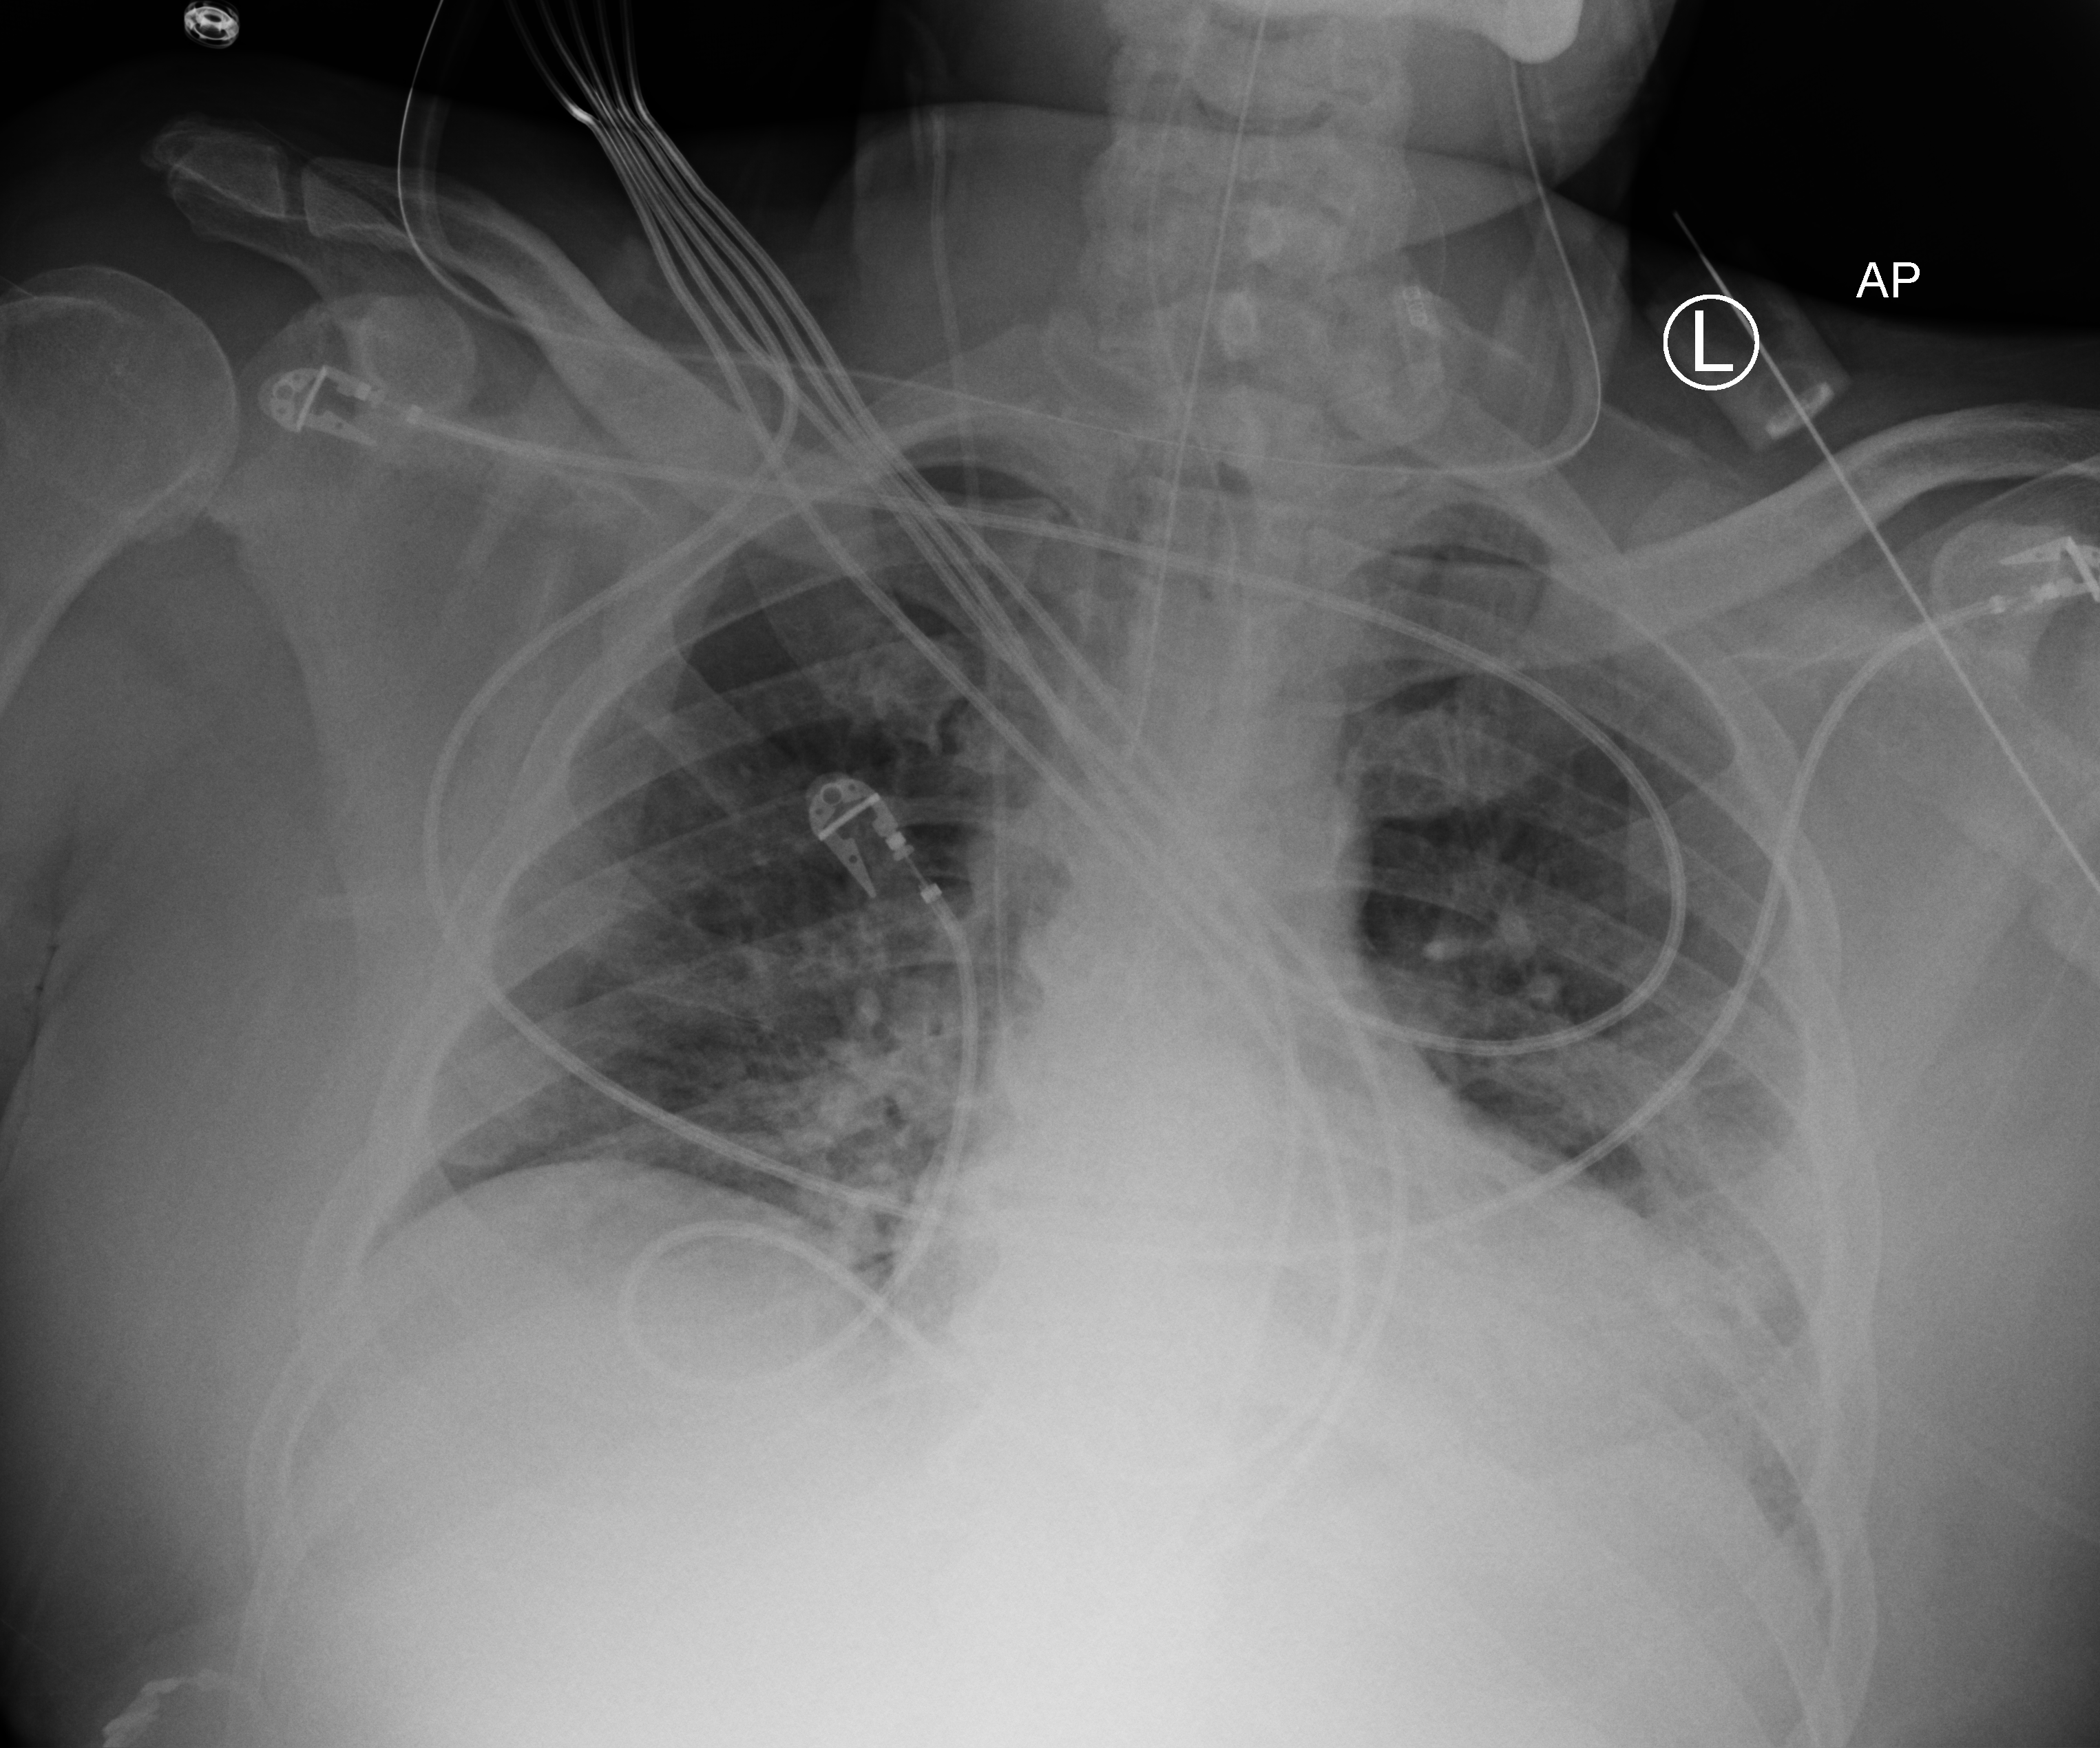
Chest X-ray (portable). Male patient hospitalised with COVID-19, age 18–59 years.
Admission-level facts for this patient (not findings on this image; timing relative to this image not recorded): mechanically ventilated during this hospital stay: yes; admitted to intensive care during this hospital stay: yes; diabetes (admission record): no.